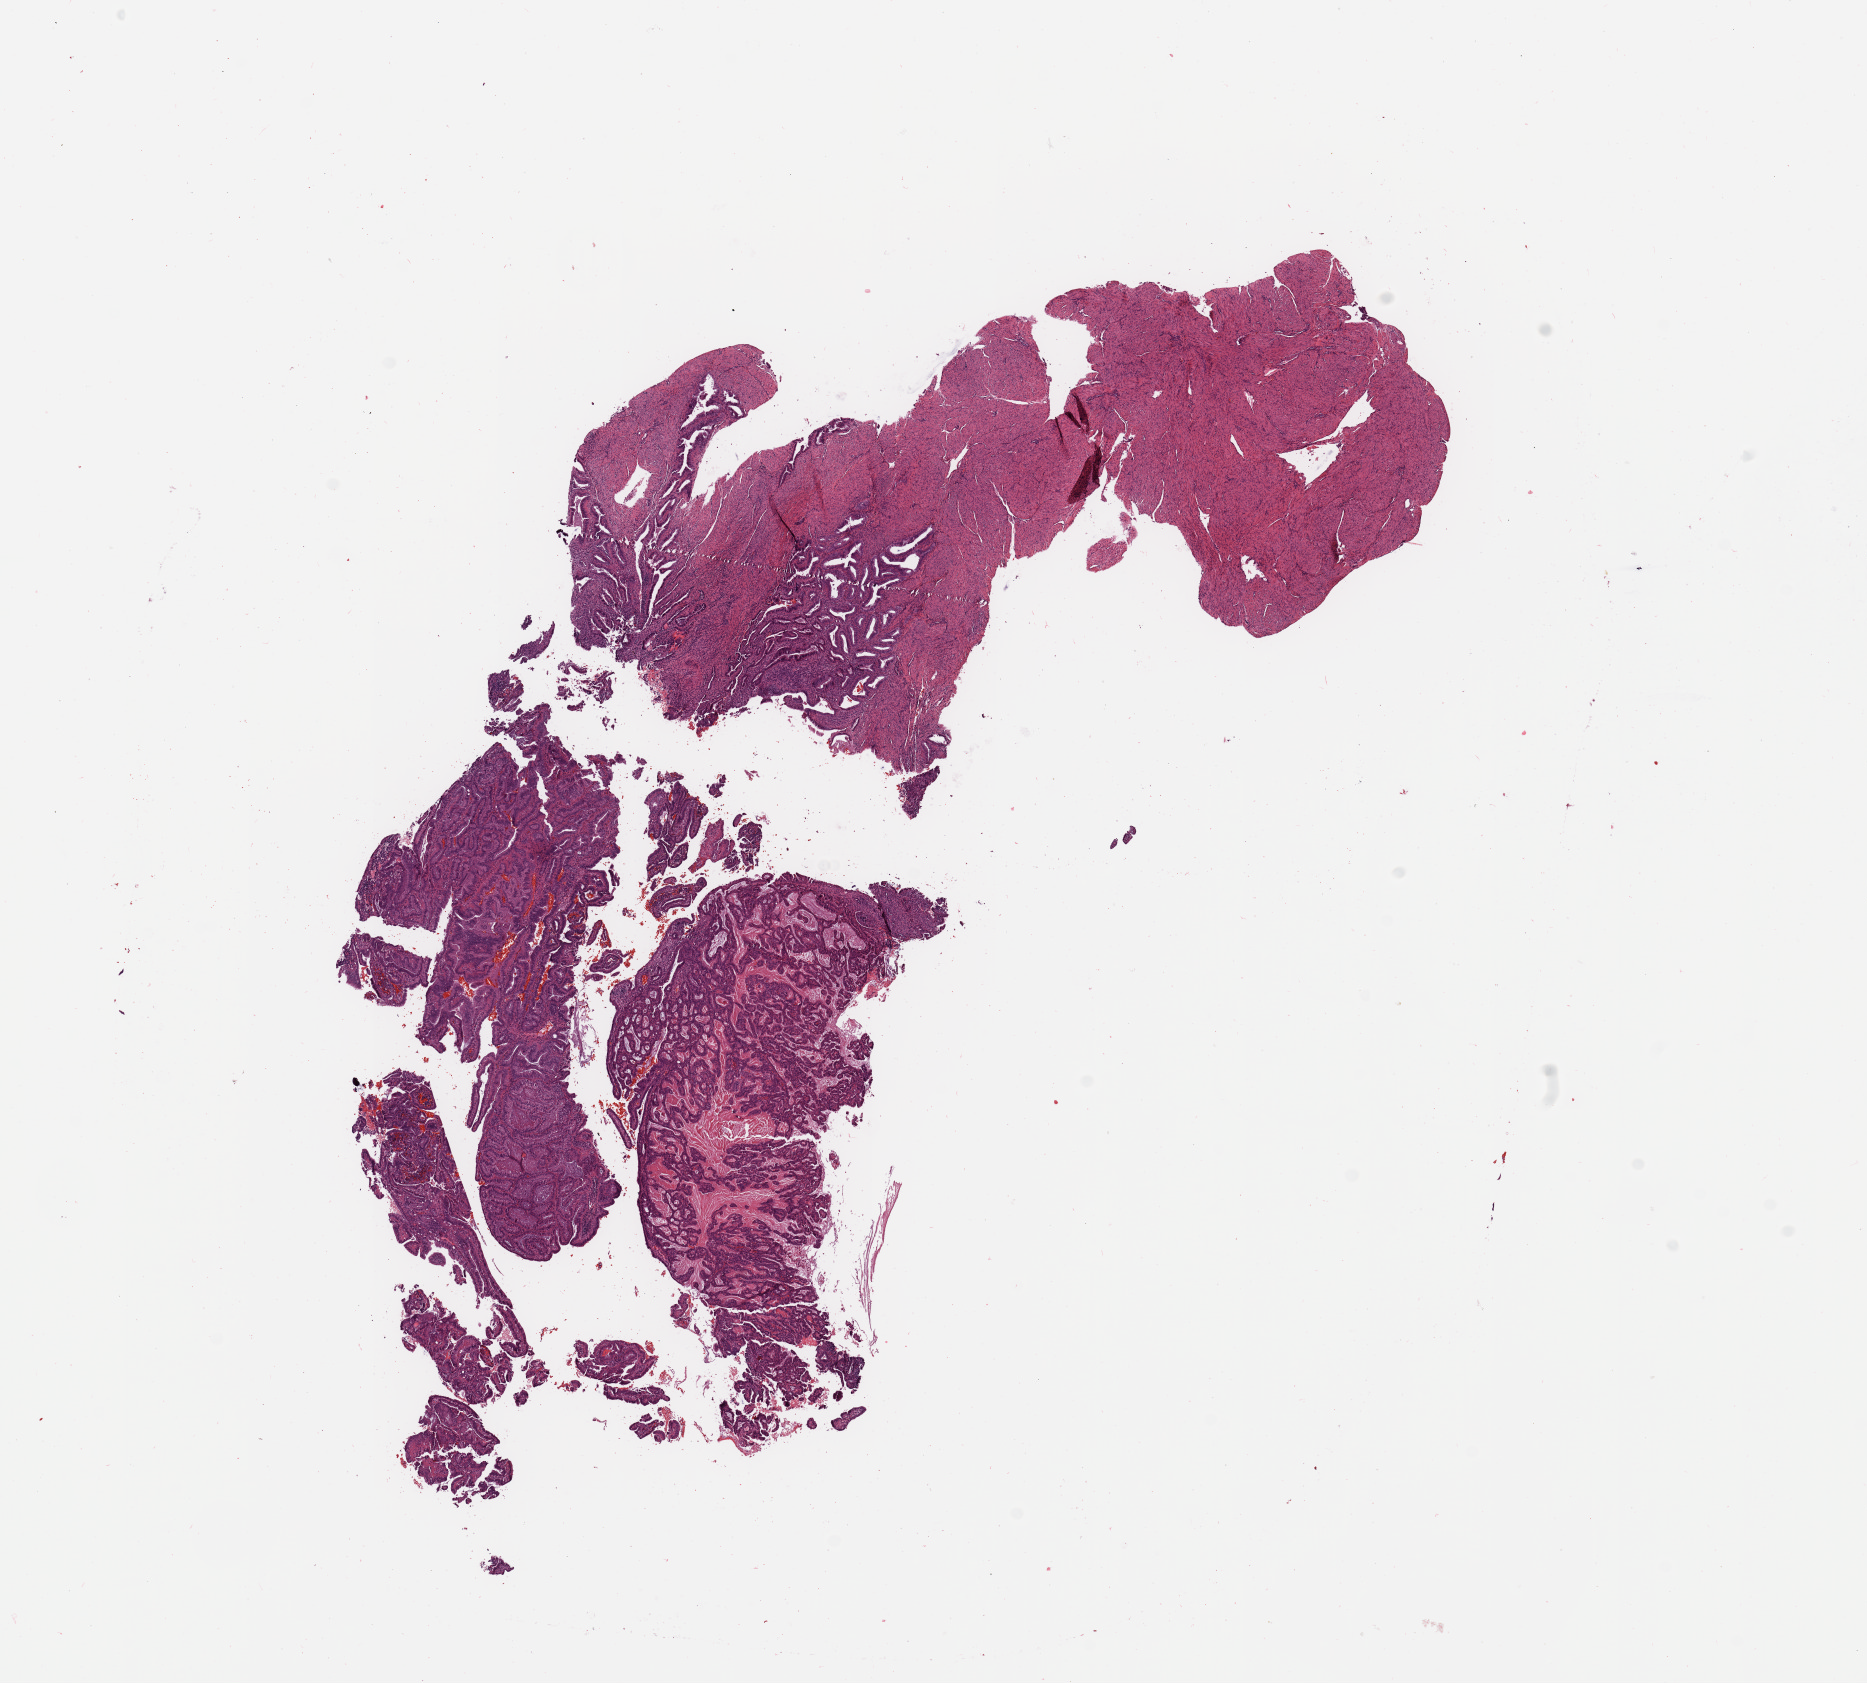
H&E-stained whole-slide image — low-resolution overview of the scanned area, about 14.8 x 13.3 mm, tumour tissue sample, sampled site: uterus. Patient: female, age 63 years. Histologic grade: G1 (well differentiated). Composition of this section per pathologist review: tumour nuclei 80%, necrosis 0%.
Histologic diagnosis: Endometrioid adenocarcinoma, NOS. AJCC pathologic stage: I.